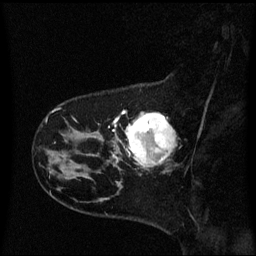
Breast MRI (dynamic contrast-enhanced), one sagittal slice; slice 14 of 60 in the series (ordered by position); dynamic contrast-enhanced series, image 2 of 3 at this slice position (ordered by acquisition); 1.5 T; TE 4.2 ms, TR 8.4 ms; 2 mm slice thickness; 256 × 256 image matrix, field of view 220 × 220 mm. Female patient, age 41 years. From the clinical record (not read from this slice): setting: breast cancer imaged before/during neoadjuvant chemotherapy; receptor status: triple-negative.
Annotated regions visible in this slice (semi-automatically segmented with operator editing):
- analysis volume of interest (the breast-tissue region the enhancement analysis was run in; not a lesion): bounding box <116,112,175,171> (left, top, right, bottom; pixels)
- tumour enhancement mask (voxels above the 70 % enhancement threshold inside the analysis volume of interest): <125,114,175,165>